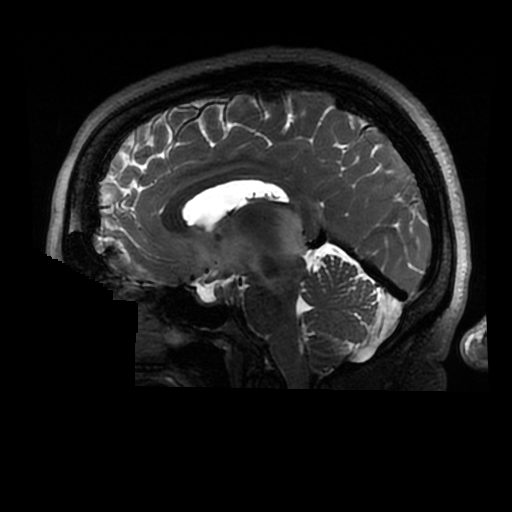
Brain MRI from a brain-tumour surgery series, one sagittal slice; position 158 of 320 along the scan axis; 0.6 mm slice thickness; 512 × 512 image matrix, field of view 240 × 240 mm. Case-level facts recorded for this patient, not image findings: histopathology: Astrocytoma; WHO grade: 2; IDH mutation: yes.
Outlined on this slice (manually delineated by an expert):
- tumour: bounding box [x1, y1, x2, y2] px = [276, 208, 304, 260]